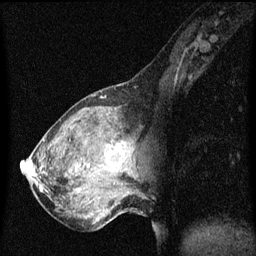
Breast MRI (dynamic contrast-enhanced), one sagittal slice; slice 22 of 60 in the series (ordered by position); dynamic contrast-enhanced series, image 2 of 3 at this slice position (ordered by acquisition); 1.5 T; TE 4.2 ms, TR 8 ms; 256 × 256 image matrix, field of view 200 × 200 mm. Female patient, age 50 years.
Annotated regions visible in this slice (semi-automatically segmented with operator editing):
- analysis volume of interest (the breast-tissue region the enhancement analysis was run in; not a lesion): bounding box [x1, y1, x2, y2] px = [91, 126, 138, 189]
- tumour enhancement mask (voxels above the 70 % enhancement threshold inside the analysis volume of interest): [108, 144, 123, 165]